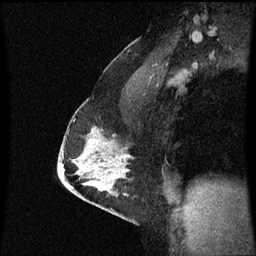
Breast MRI (dynamic contrast-enhanced), one sagittal slice. Slice 39 of 60 in the series (ordered by position). Dynamic contrast-enhanced series, image 2 of 3 at this slice position (ordered by acquisition). 1.5 T. TE 4.2 ms, TR 8.9 ms. 2 mm slice thickness. 256 × 256 image matrix, field of view 200 × 200 mm. Patient: female, 47 years. From the clinical record (not read from this slice): setting: breast cancer imaged before/during neoadjuvant chemotherapy; receptor status: HR-positive, HER2-negative.
Structures marked on this image (semi-automatic segmentation, software-assisted and operator-edited):
- analysis volume of interest (the breast-tissue region the enhancement analysis was run in; not a lesion): box from (x=60, y=110) to (x=132, y=209) px
- tumour enhancement mask (voxels above the 70 % enhancement threshold inside the analysis volume of interest): (x=90, y=140)–(x=127, y=191)